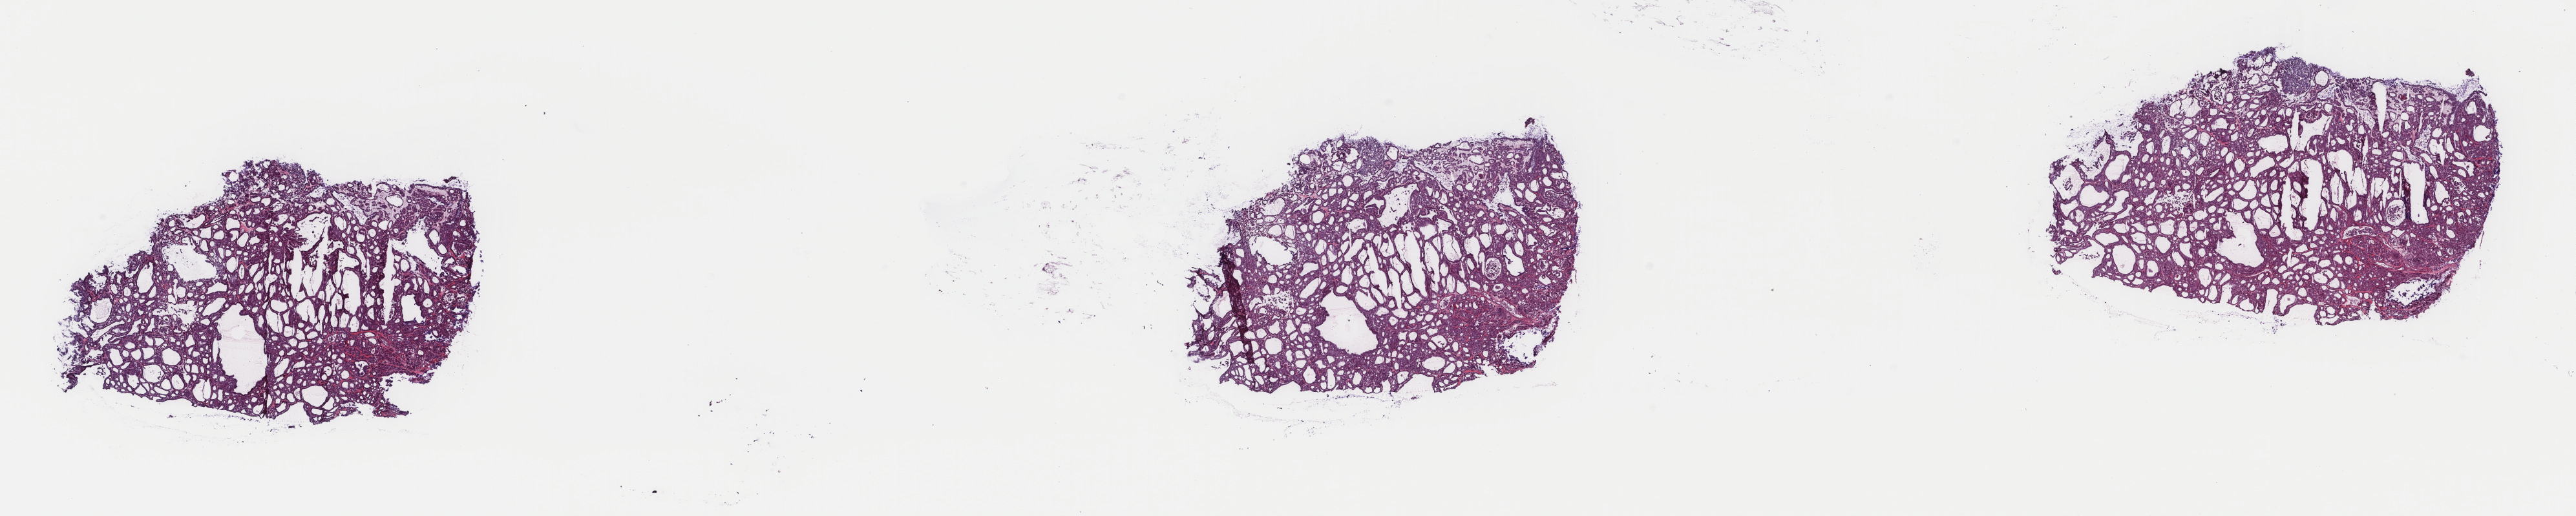
Digitized Hematoxylin and eosin (H&E) stained tissue section (whole slide) — low-resolution overview of the scanned area, about 31.6 x 6.3 mm (acquisition: 40x scan). Frozen section from the top of the tissue portion. Sample: primary tumour, thyroid. Female patient; age at initial diagnosis 66 years. Slide review estimates, as recorded: tumour cells 100%, tumour nuclei 88%, normal cells 0%, stromal cells 0%, necrosis 0%. Infiltration values recorded for this section: lymphocyte infiltration 0%, monocyte infiltration 0%, neutrophil infiltration 0%.
Lymph nodes positive (case pathology): 0 of 1 examined. Histologic diagnosis: Papillary carcinoma, follicular variant (thyroid gland). AJCC pathologic stage: I (7th edition).